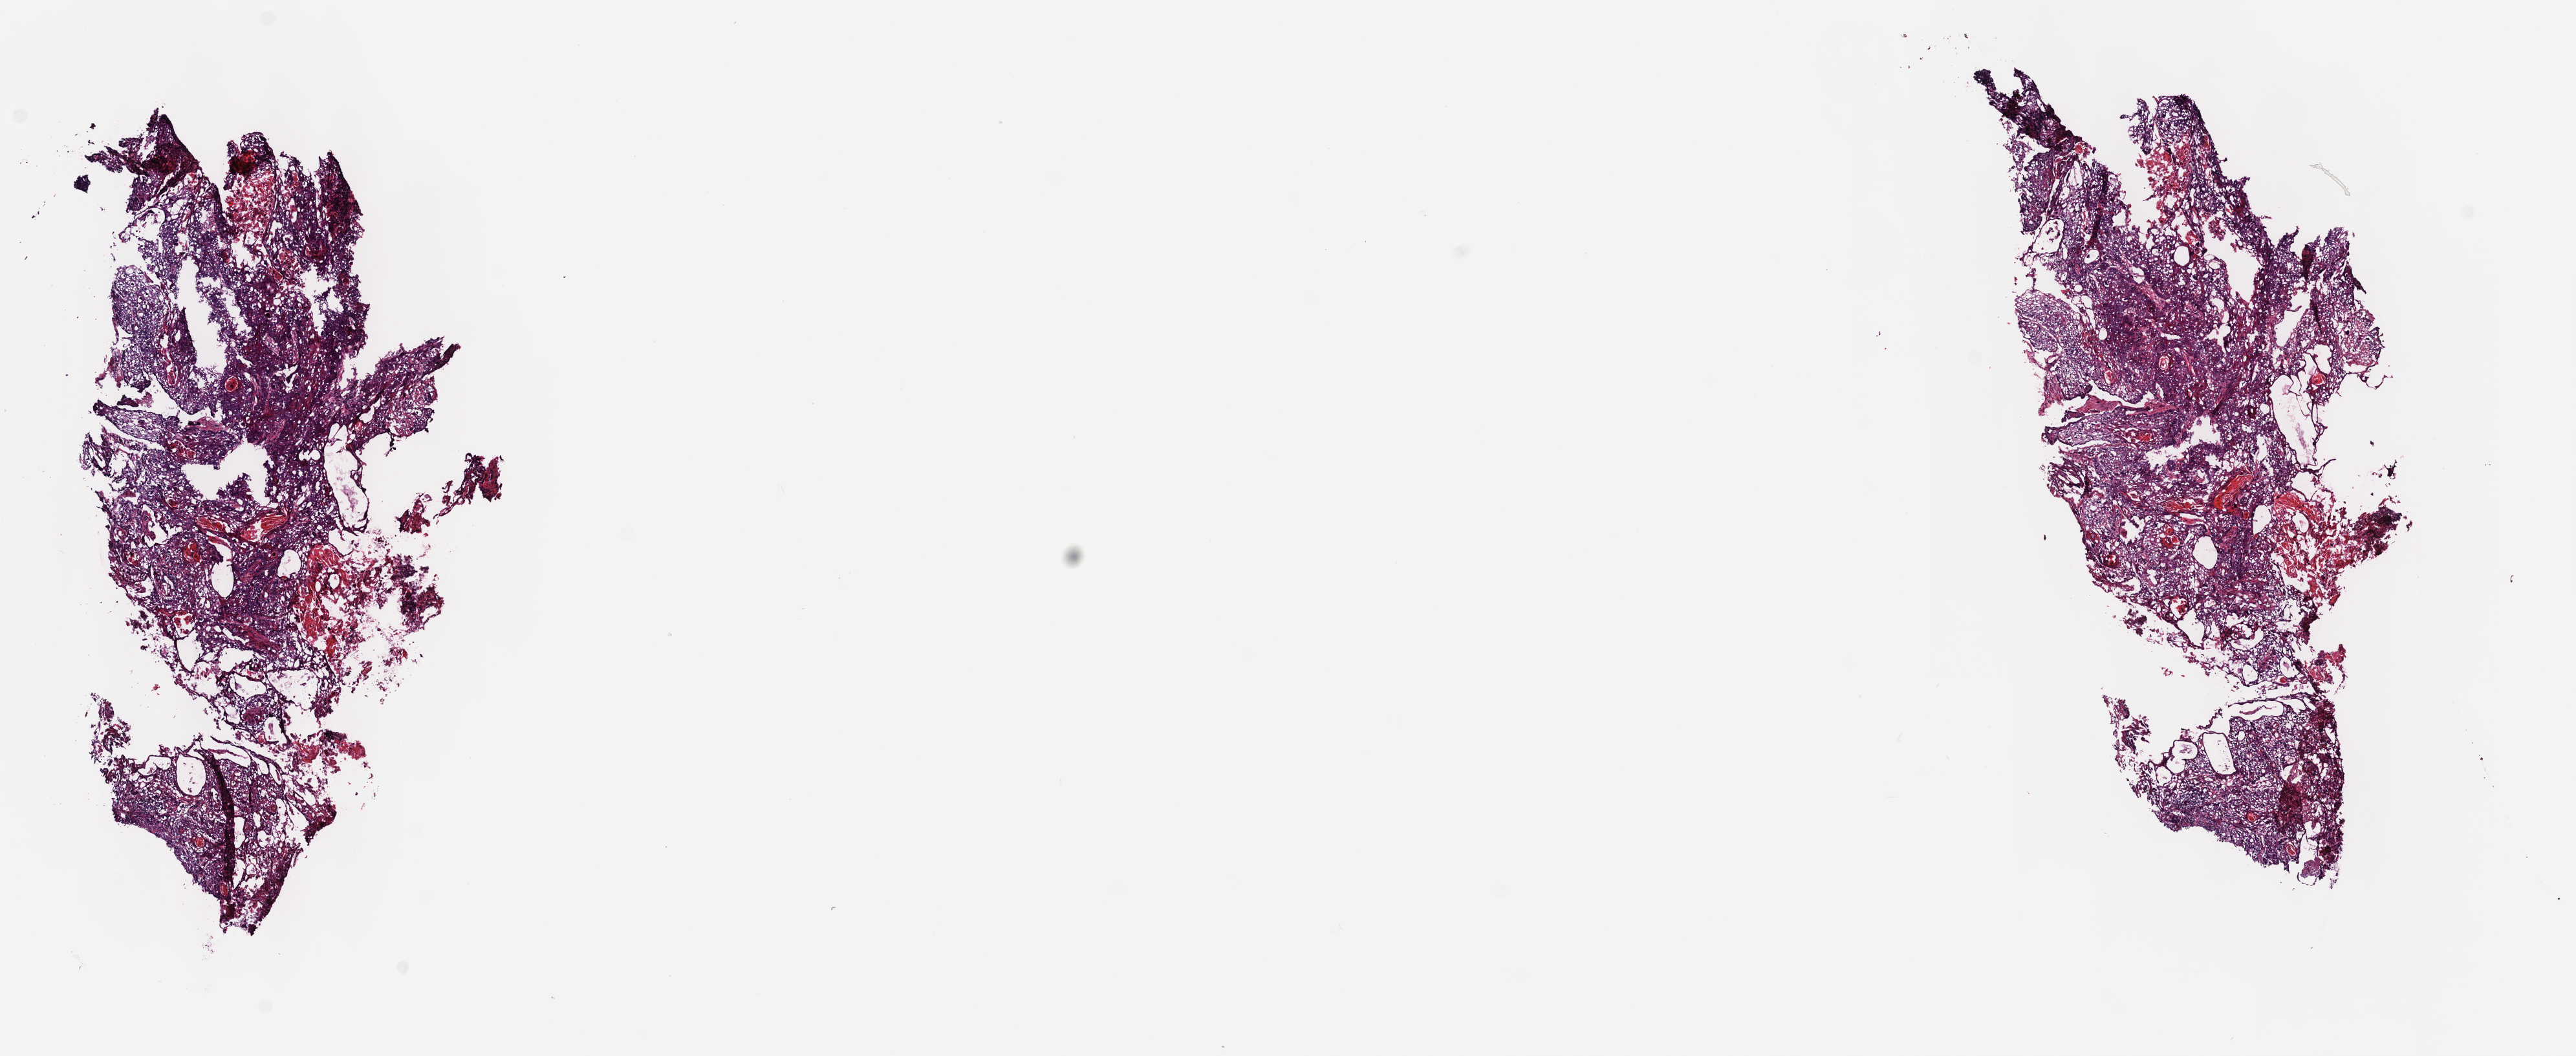
H&E whole-slide image — low-resolution overview of the scanned area, about 16.1 x 6.6 mm (slide scanned at 40x), frozen section, cervix, primary tumour sample. Female, age 43 years at initial diagnosis.
Histologic diagnosis: Squamous cell carcinoma, NOS (cervix uteri).